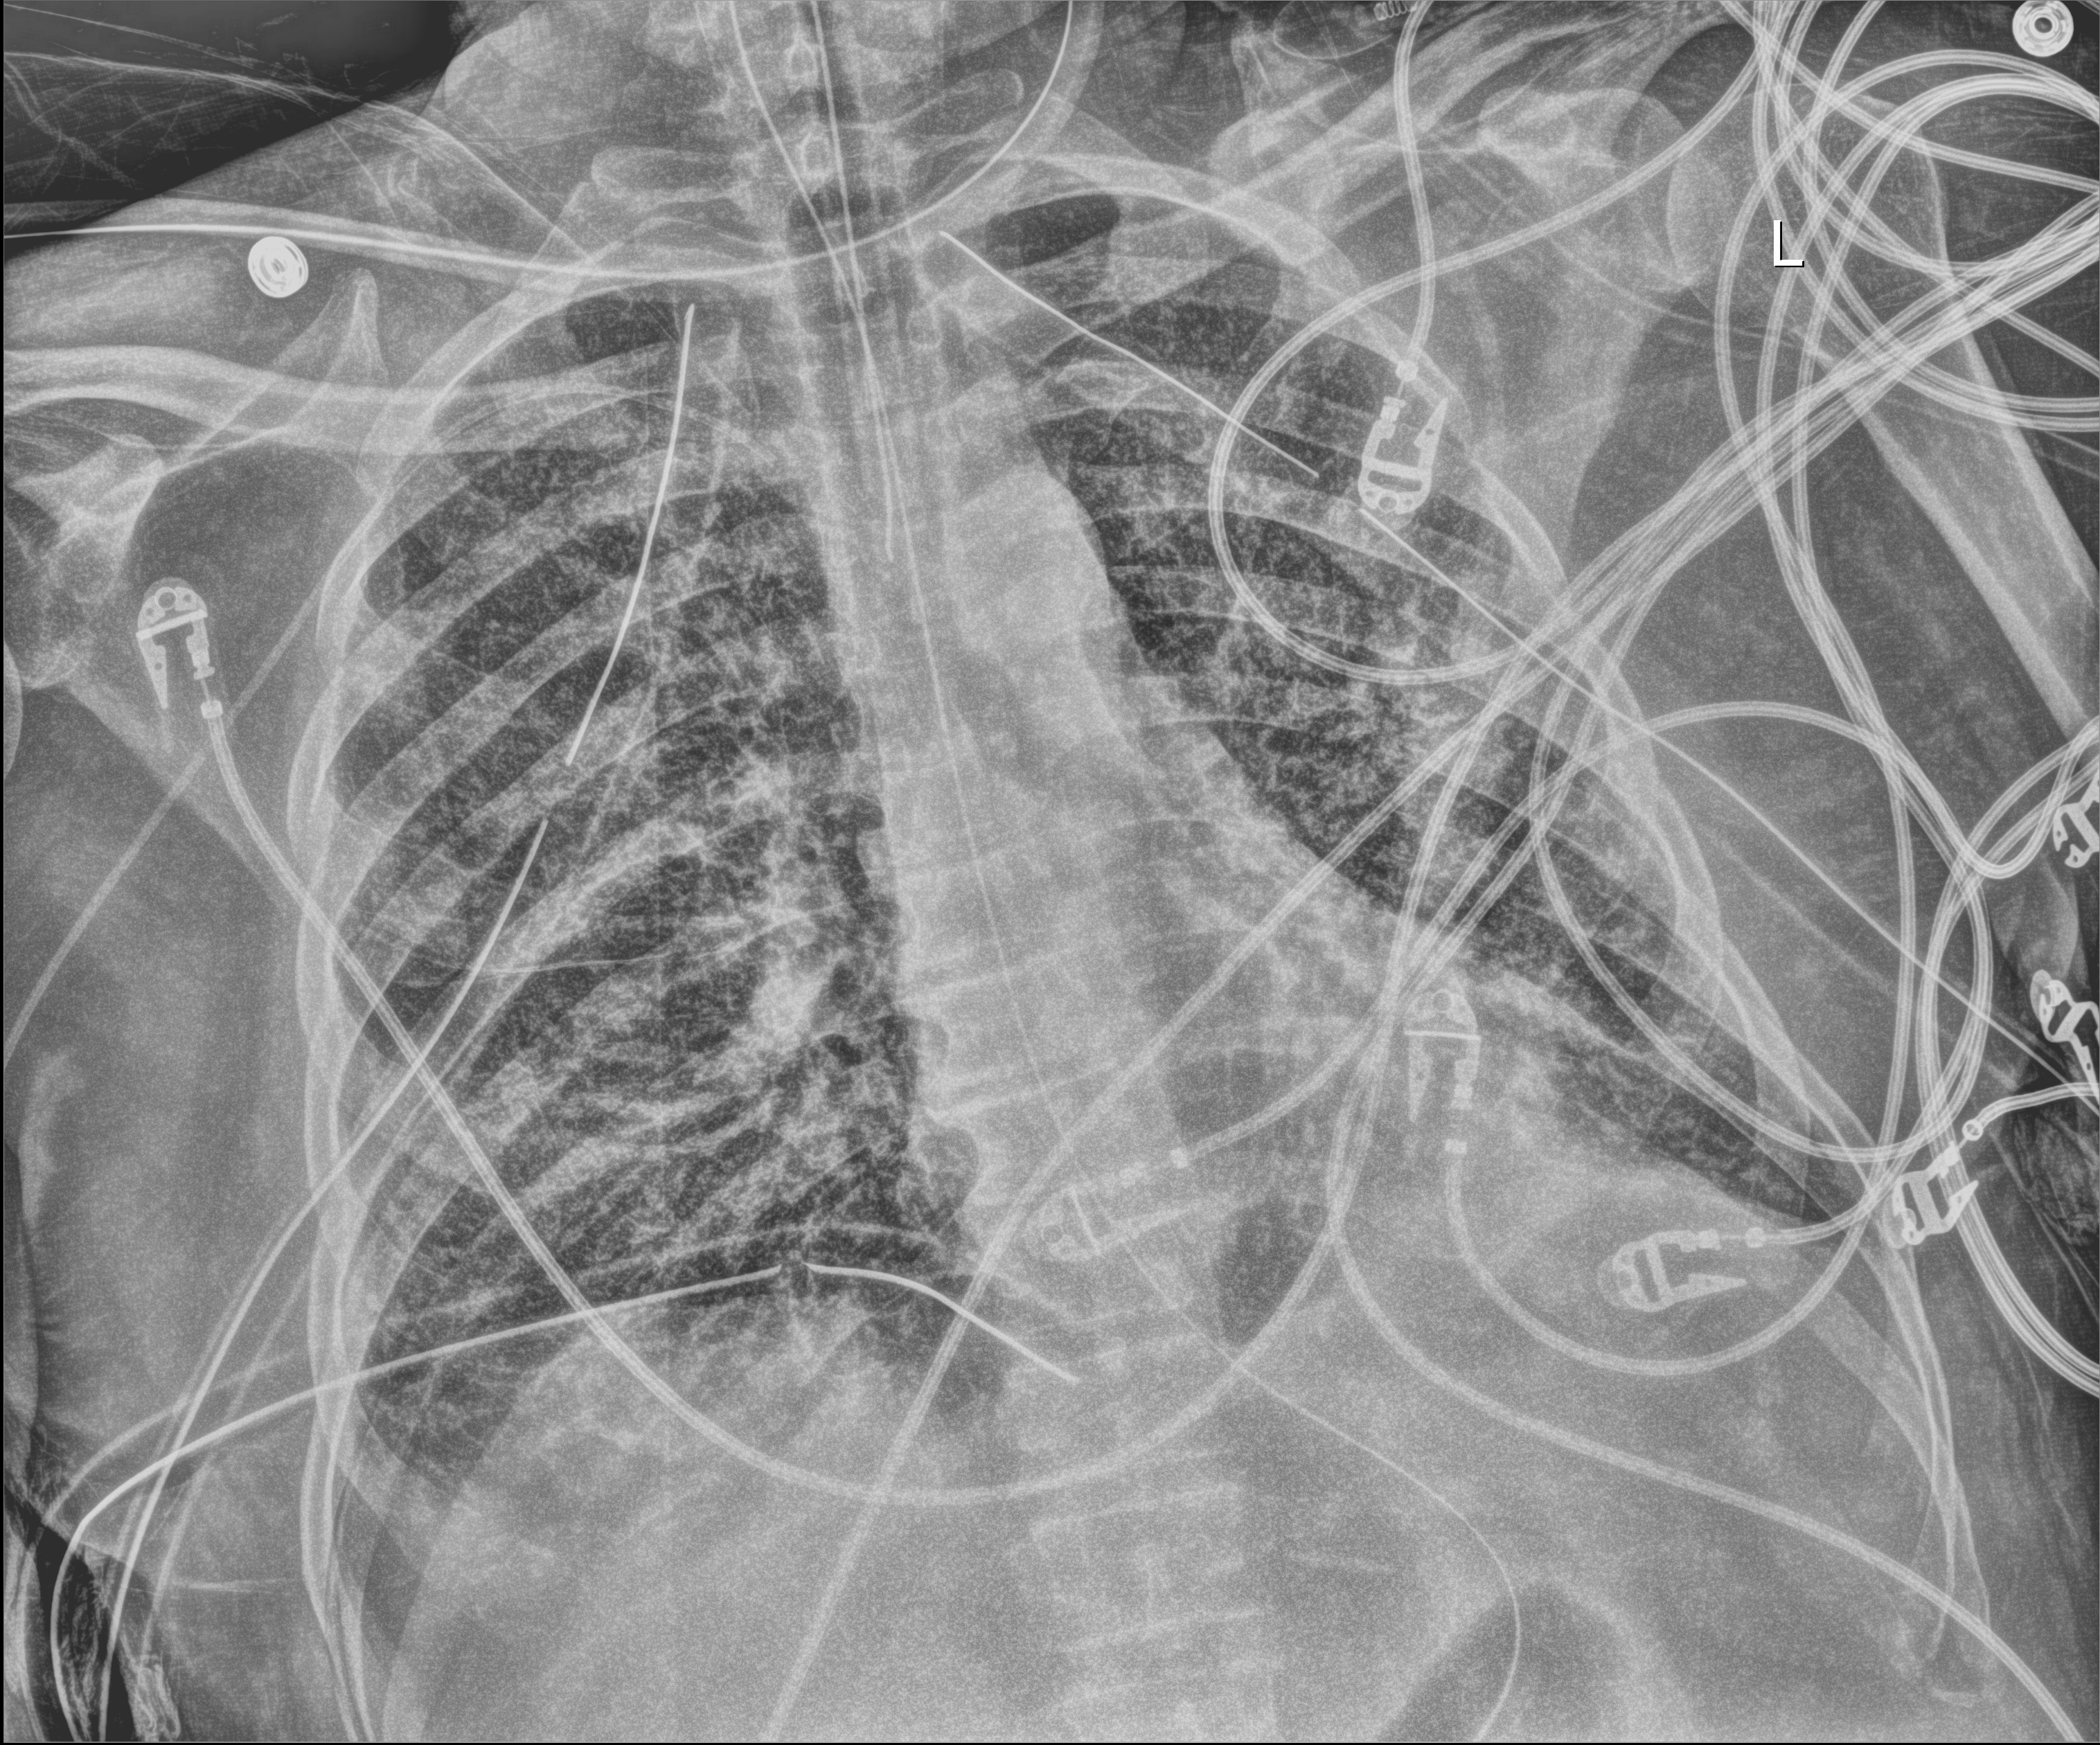
Bedside chest radiograph (digital radiography). Patient hospitalised with COVID-19; male, aged 18–59 years.
From the hospital-stay record, not from the radiograph (when in the stay this image was taken is not recorded): length of hospital stay: 83 days; admitted to intensive care during this hospital stay: yes; mechanically ventilated during this hospital stay: yes.